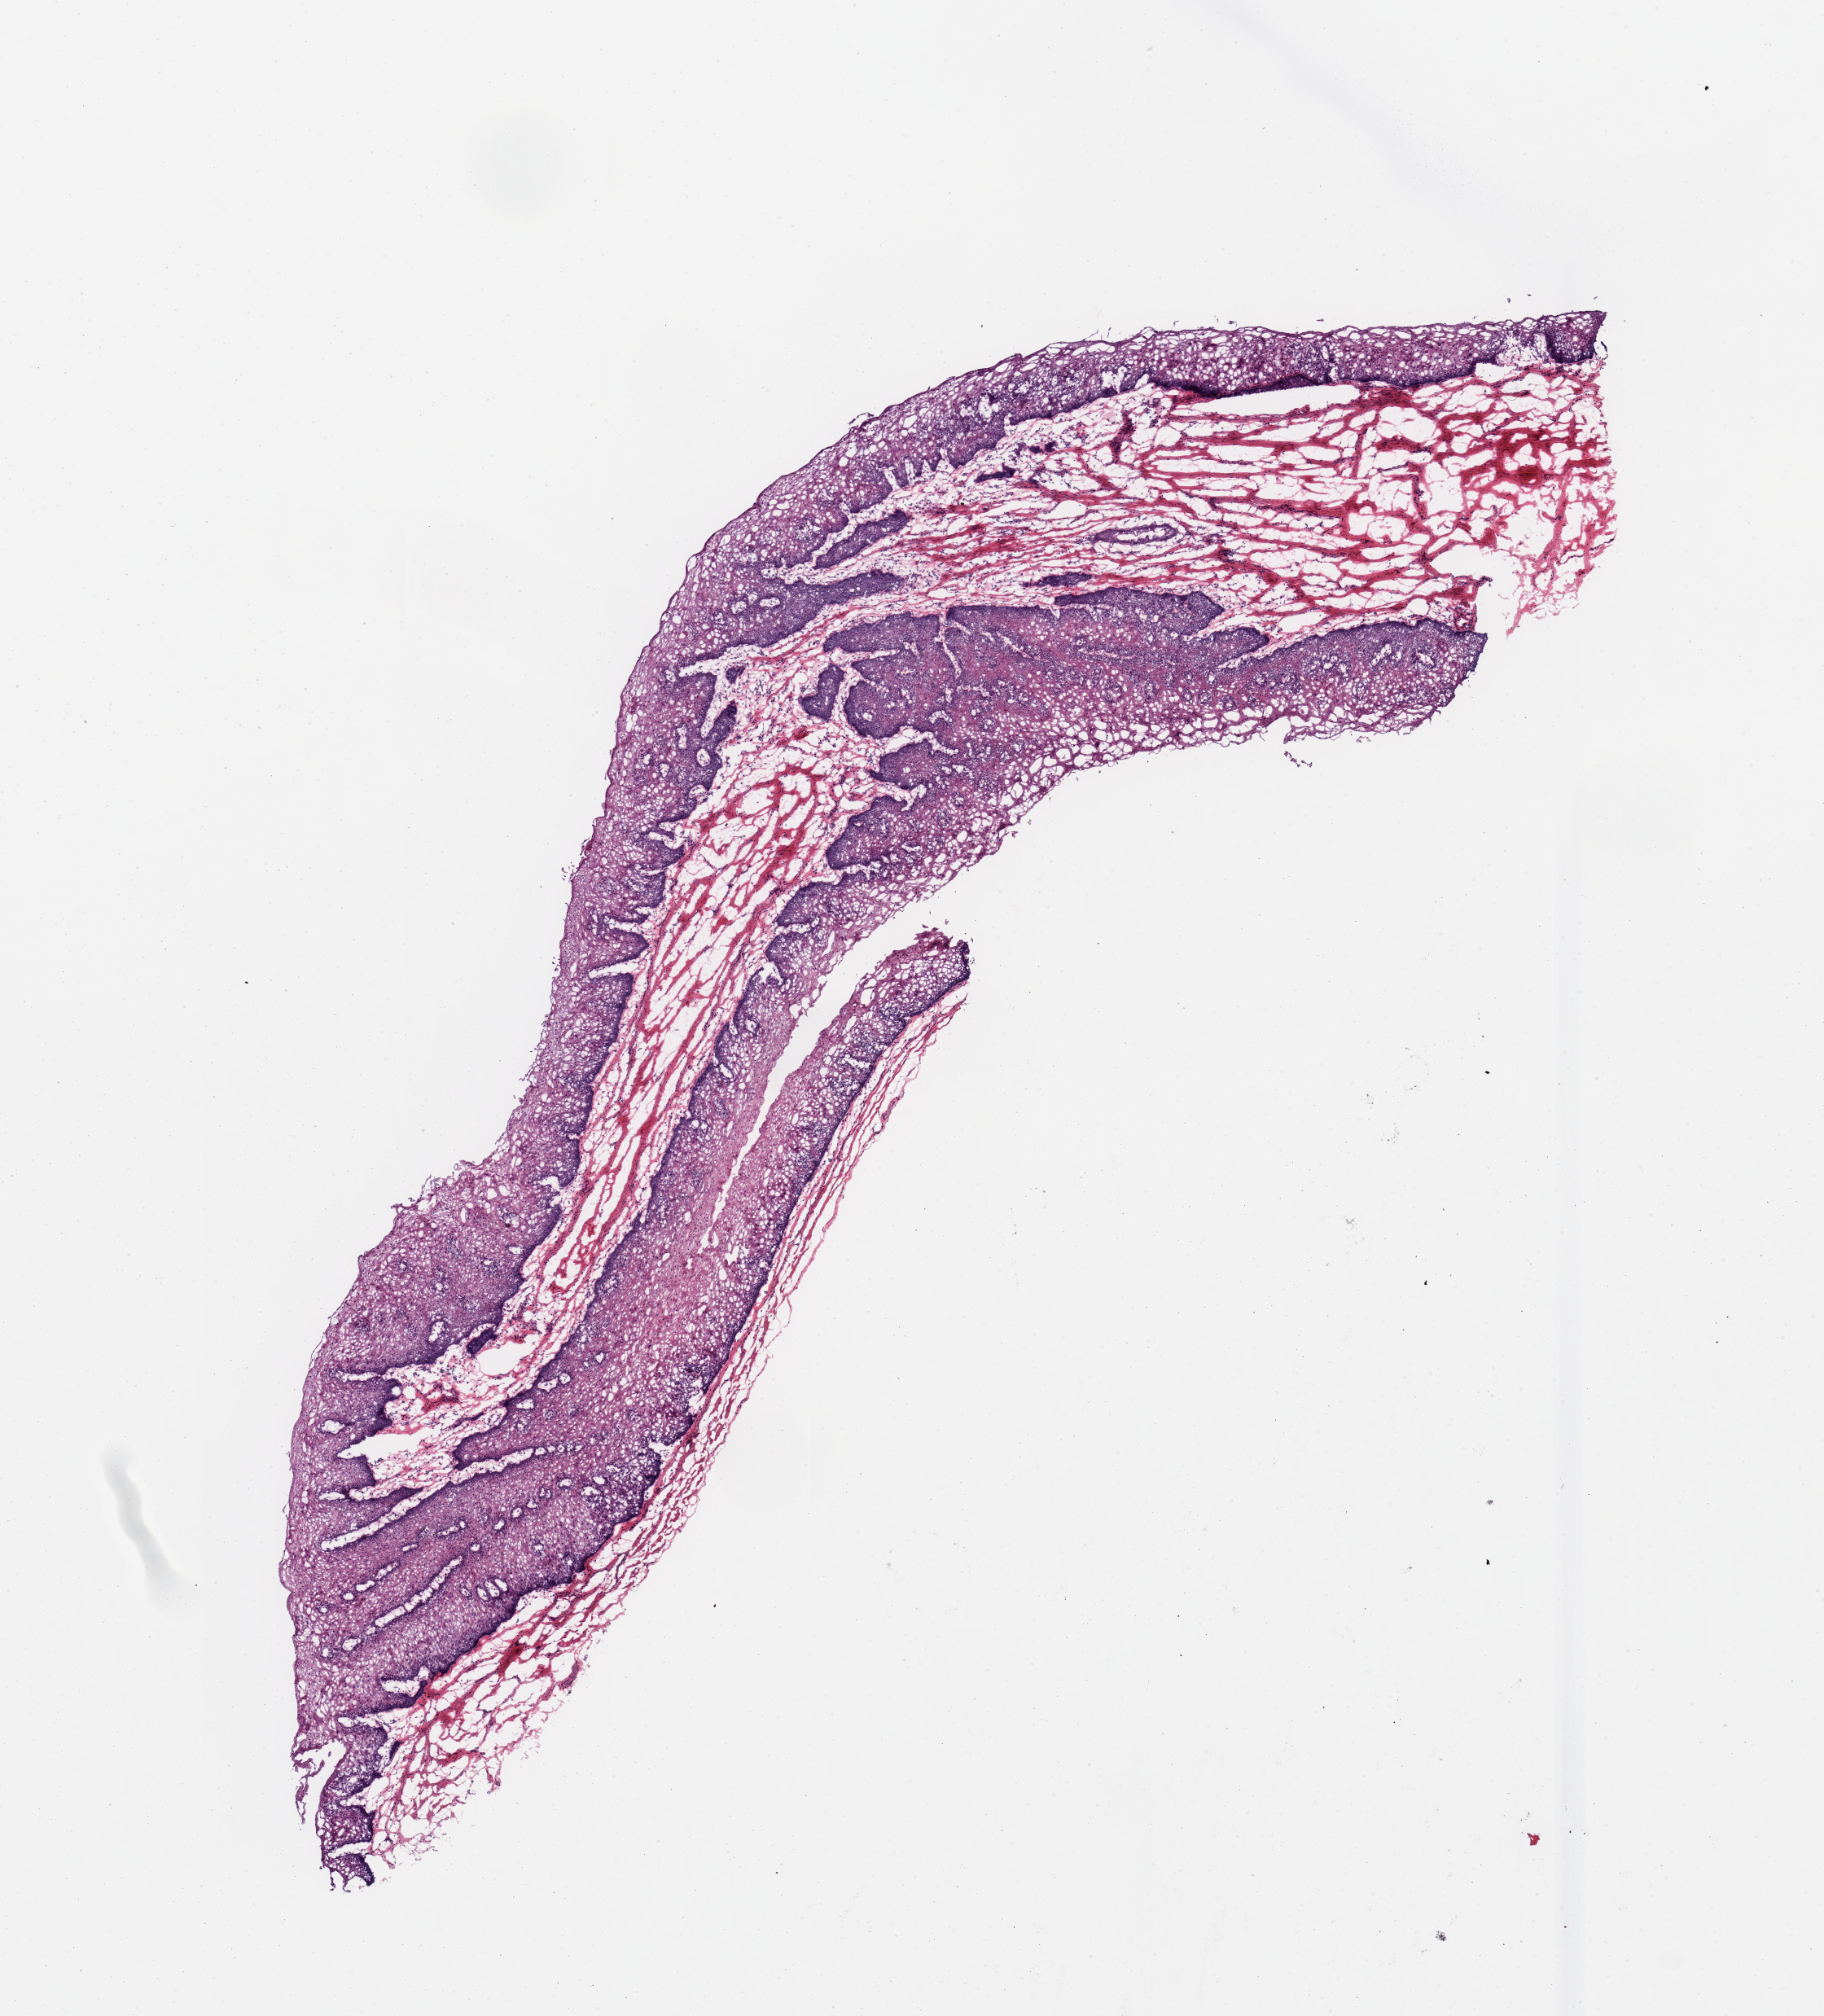
Whole-slide image, hematoxylin and eosin (H&E) stain — a low-resolution overview of the entire scanned area, about 8.9 x 9.8 mm, frozen section (dry ice), section of esophageal mucous membrane (target tissue), tissue donor sample. Female donor.
• review note (as recorded): 1 piece; squamous mucosa without submucosa; no sign of crystalline contaminants